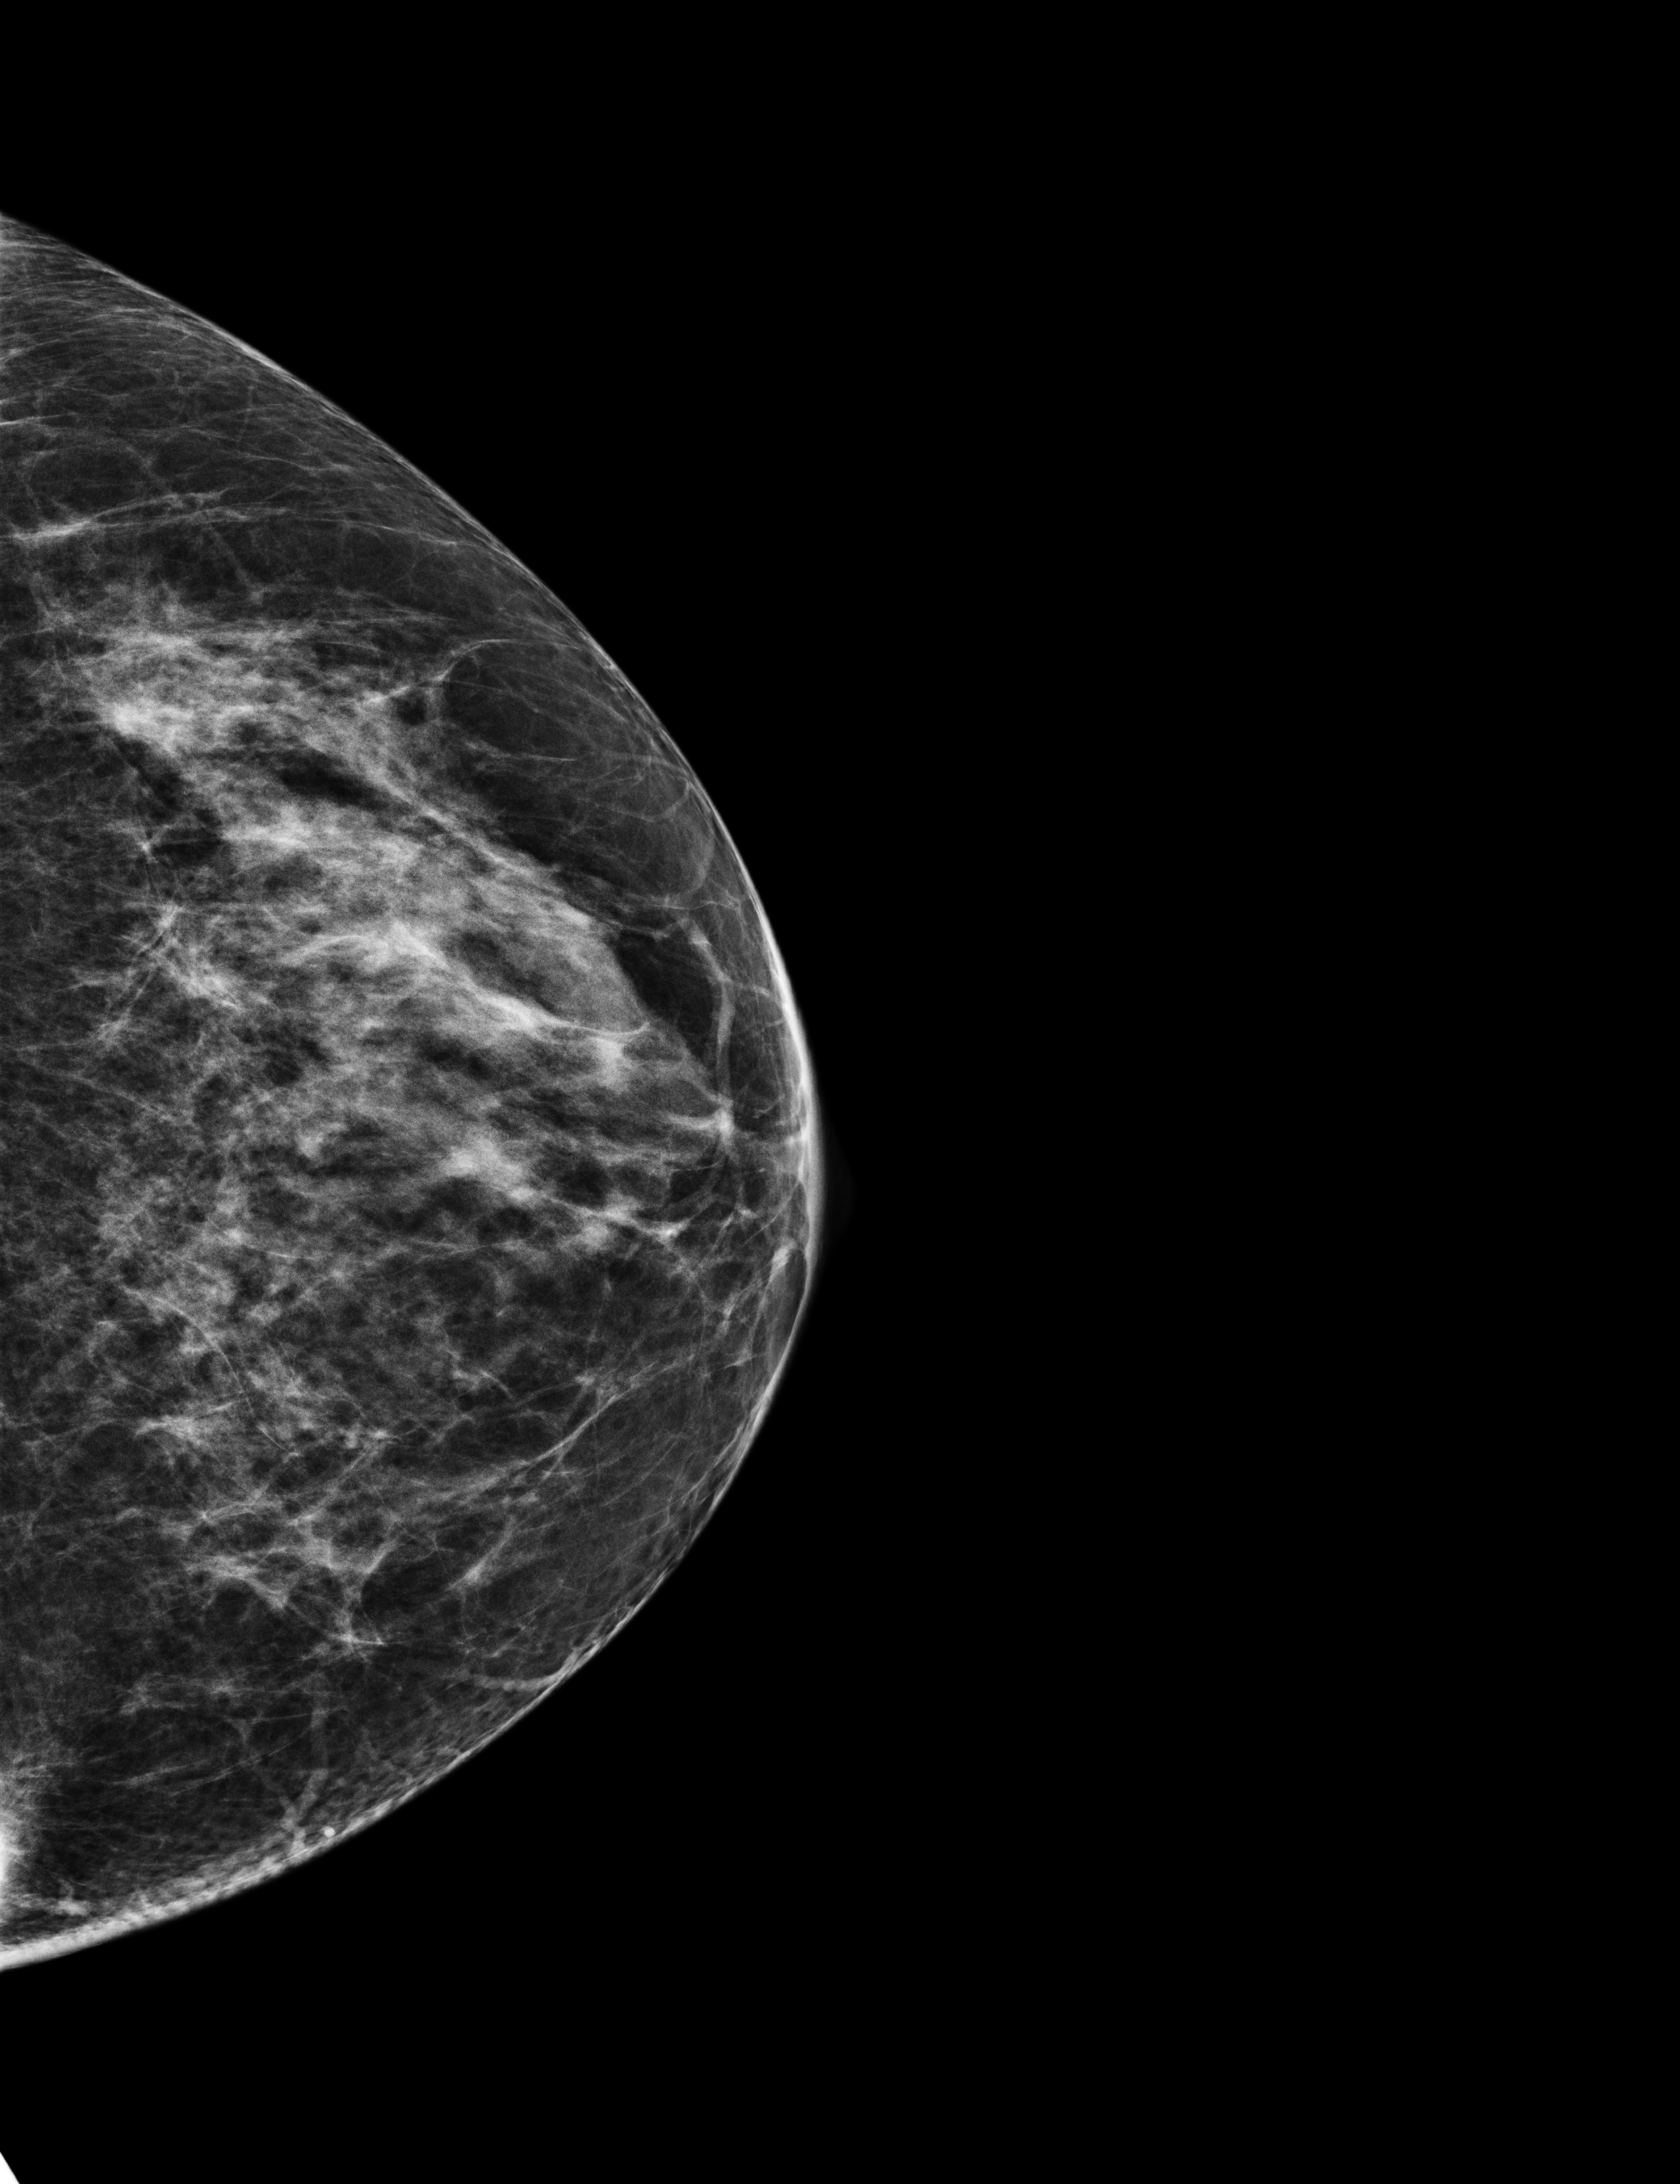
Annual screening mammography examination, compressed breast thickness 46 mm.
Image type: full-field digital mammogram. Breast: left. Projection: craniocaudal (CC) view.